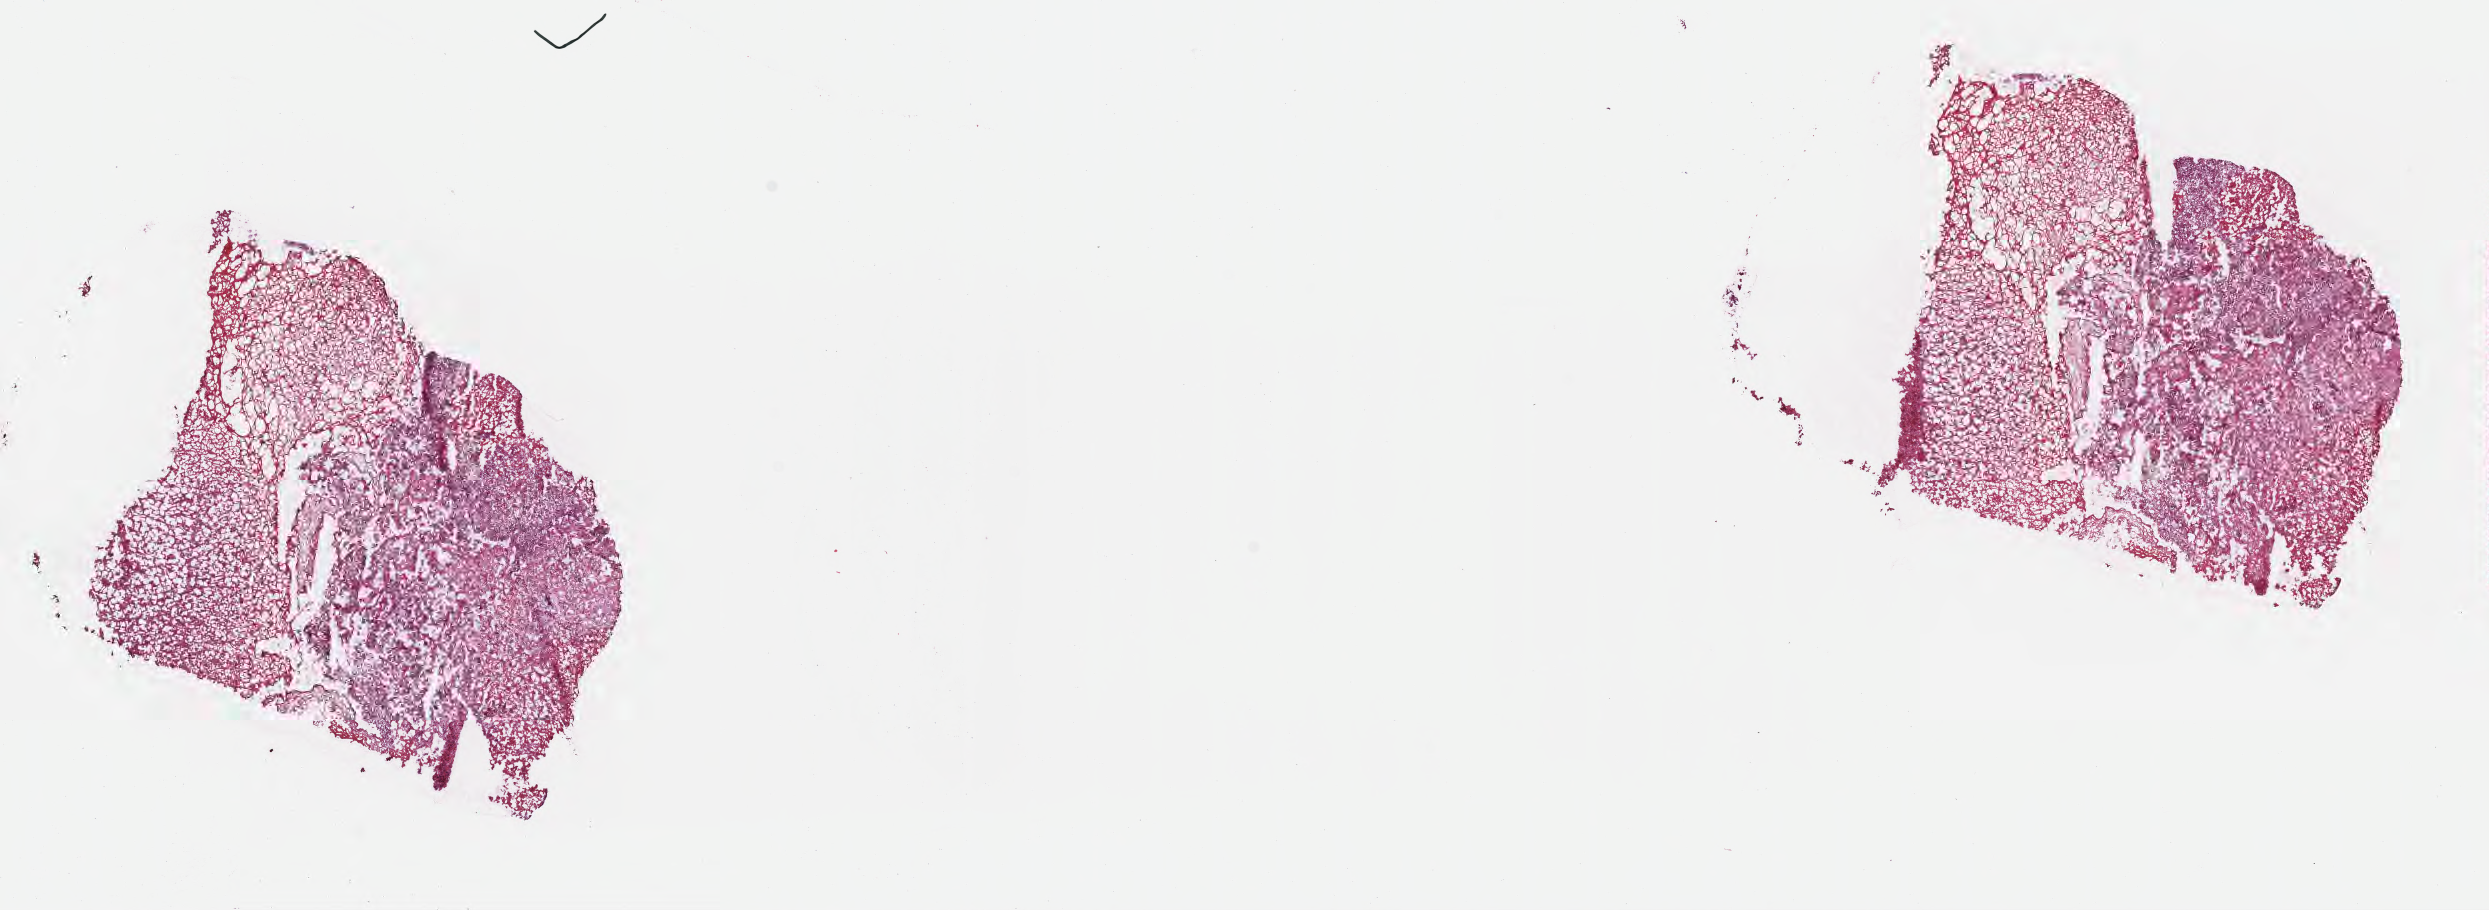
Hematoxylin and eosin (H&E) whole-slide image, shown as a low-resolution overview of the whole scanned area (about 20.1 x 7.4 mm); frozen section (tissue freezing medium); primary tumor; site: breast. Female, age 46 years at initial diagnosis. Tumor grade: G3 (poorly differentiated). Composition of this section per pathologist review: tumor cells 20%, tumor nuclei 70%, stromal cells 80%, necrosis 0%, normal cells 0%. Inflammatory infiltration, as recorded: lymphocyte infiltration 0%, monocyte infiltration 0%, neutrophil infiltration 0%.
Diagnosis: Metaplastic carcinoma, NOS. AJCC pathologic stage: Stage IIB.